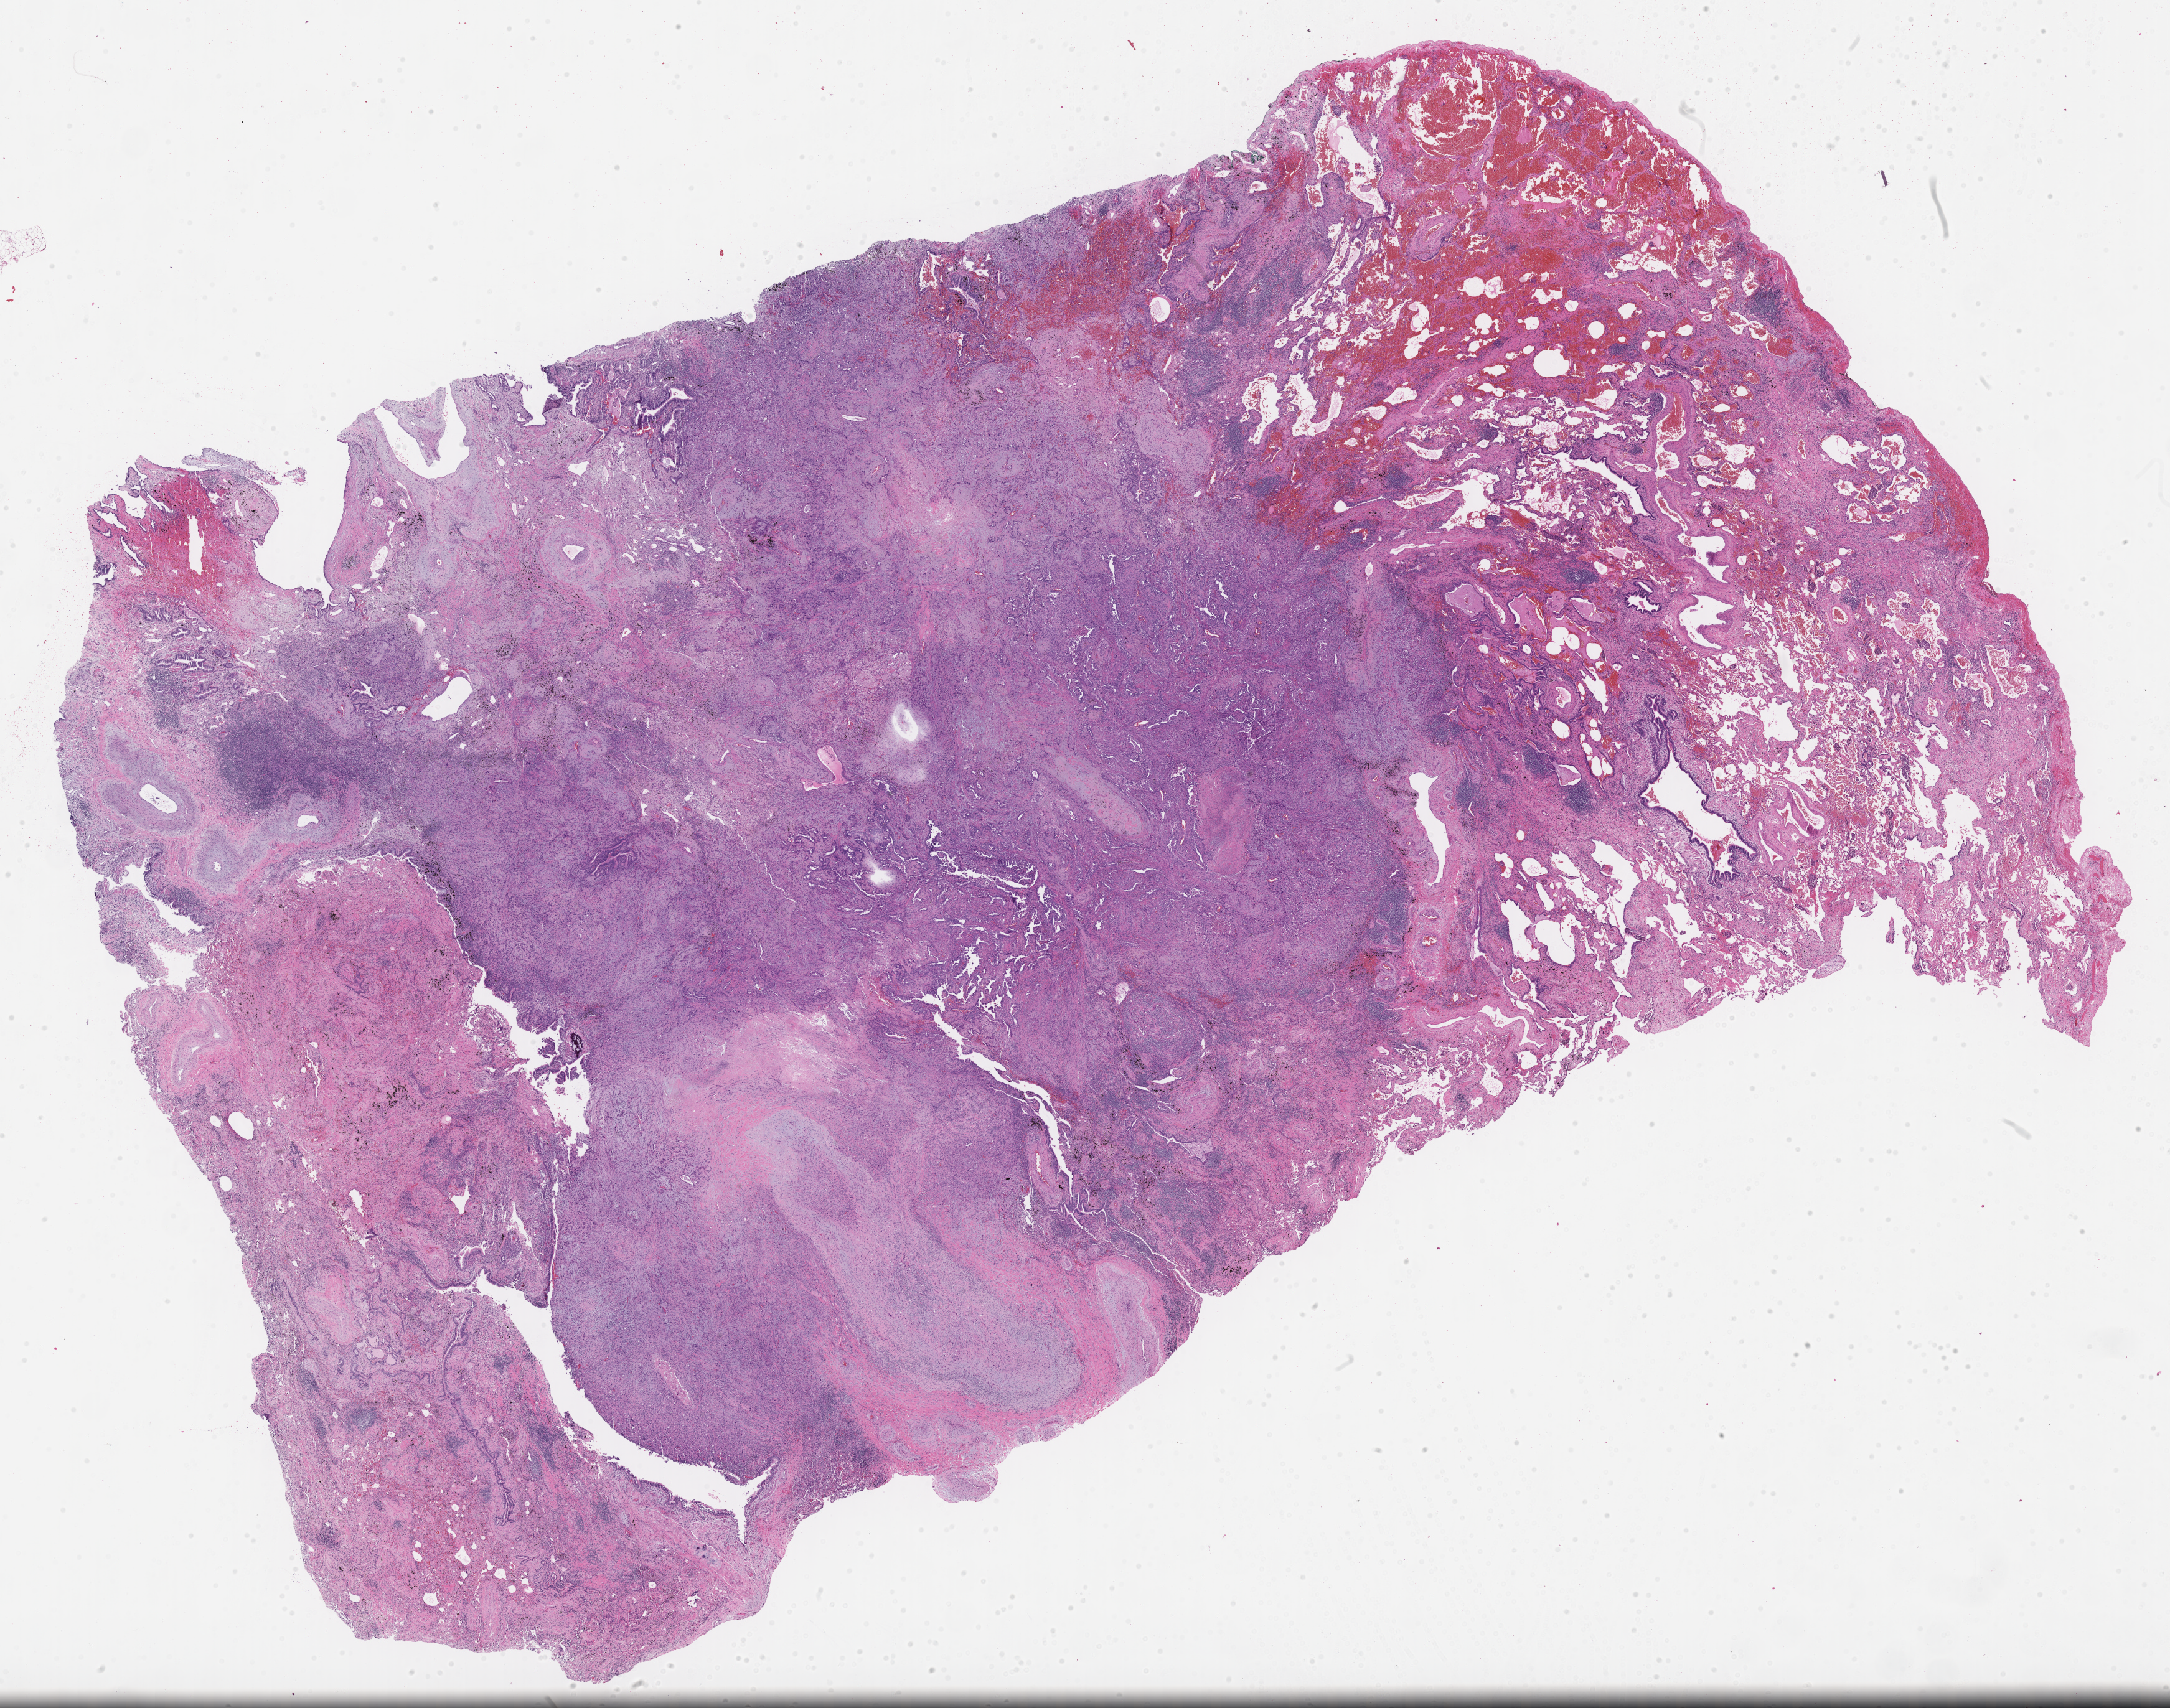
Whole-slide image, H&E stain — low-resolution overview of the scanned area, about 28.1 x 22.1 mm, formalin-fixed paraffin-embedded section, primary tumor, anatomic site: lower lobe of left lung. Male patient; age at initial diagnosis 72 years.
Diagnosis: Solid carcinoma, NOS.